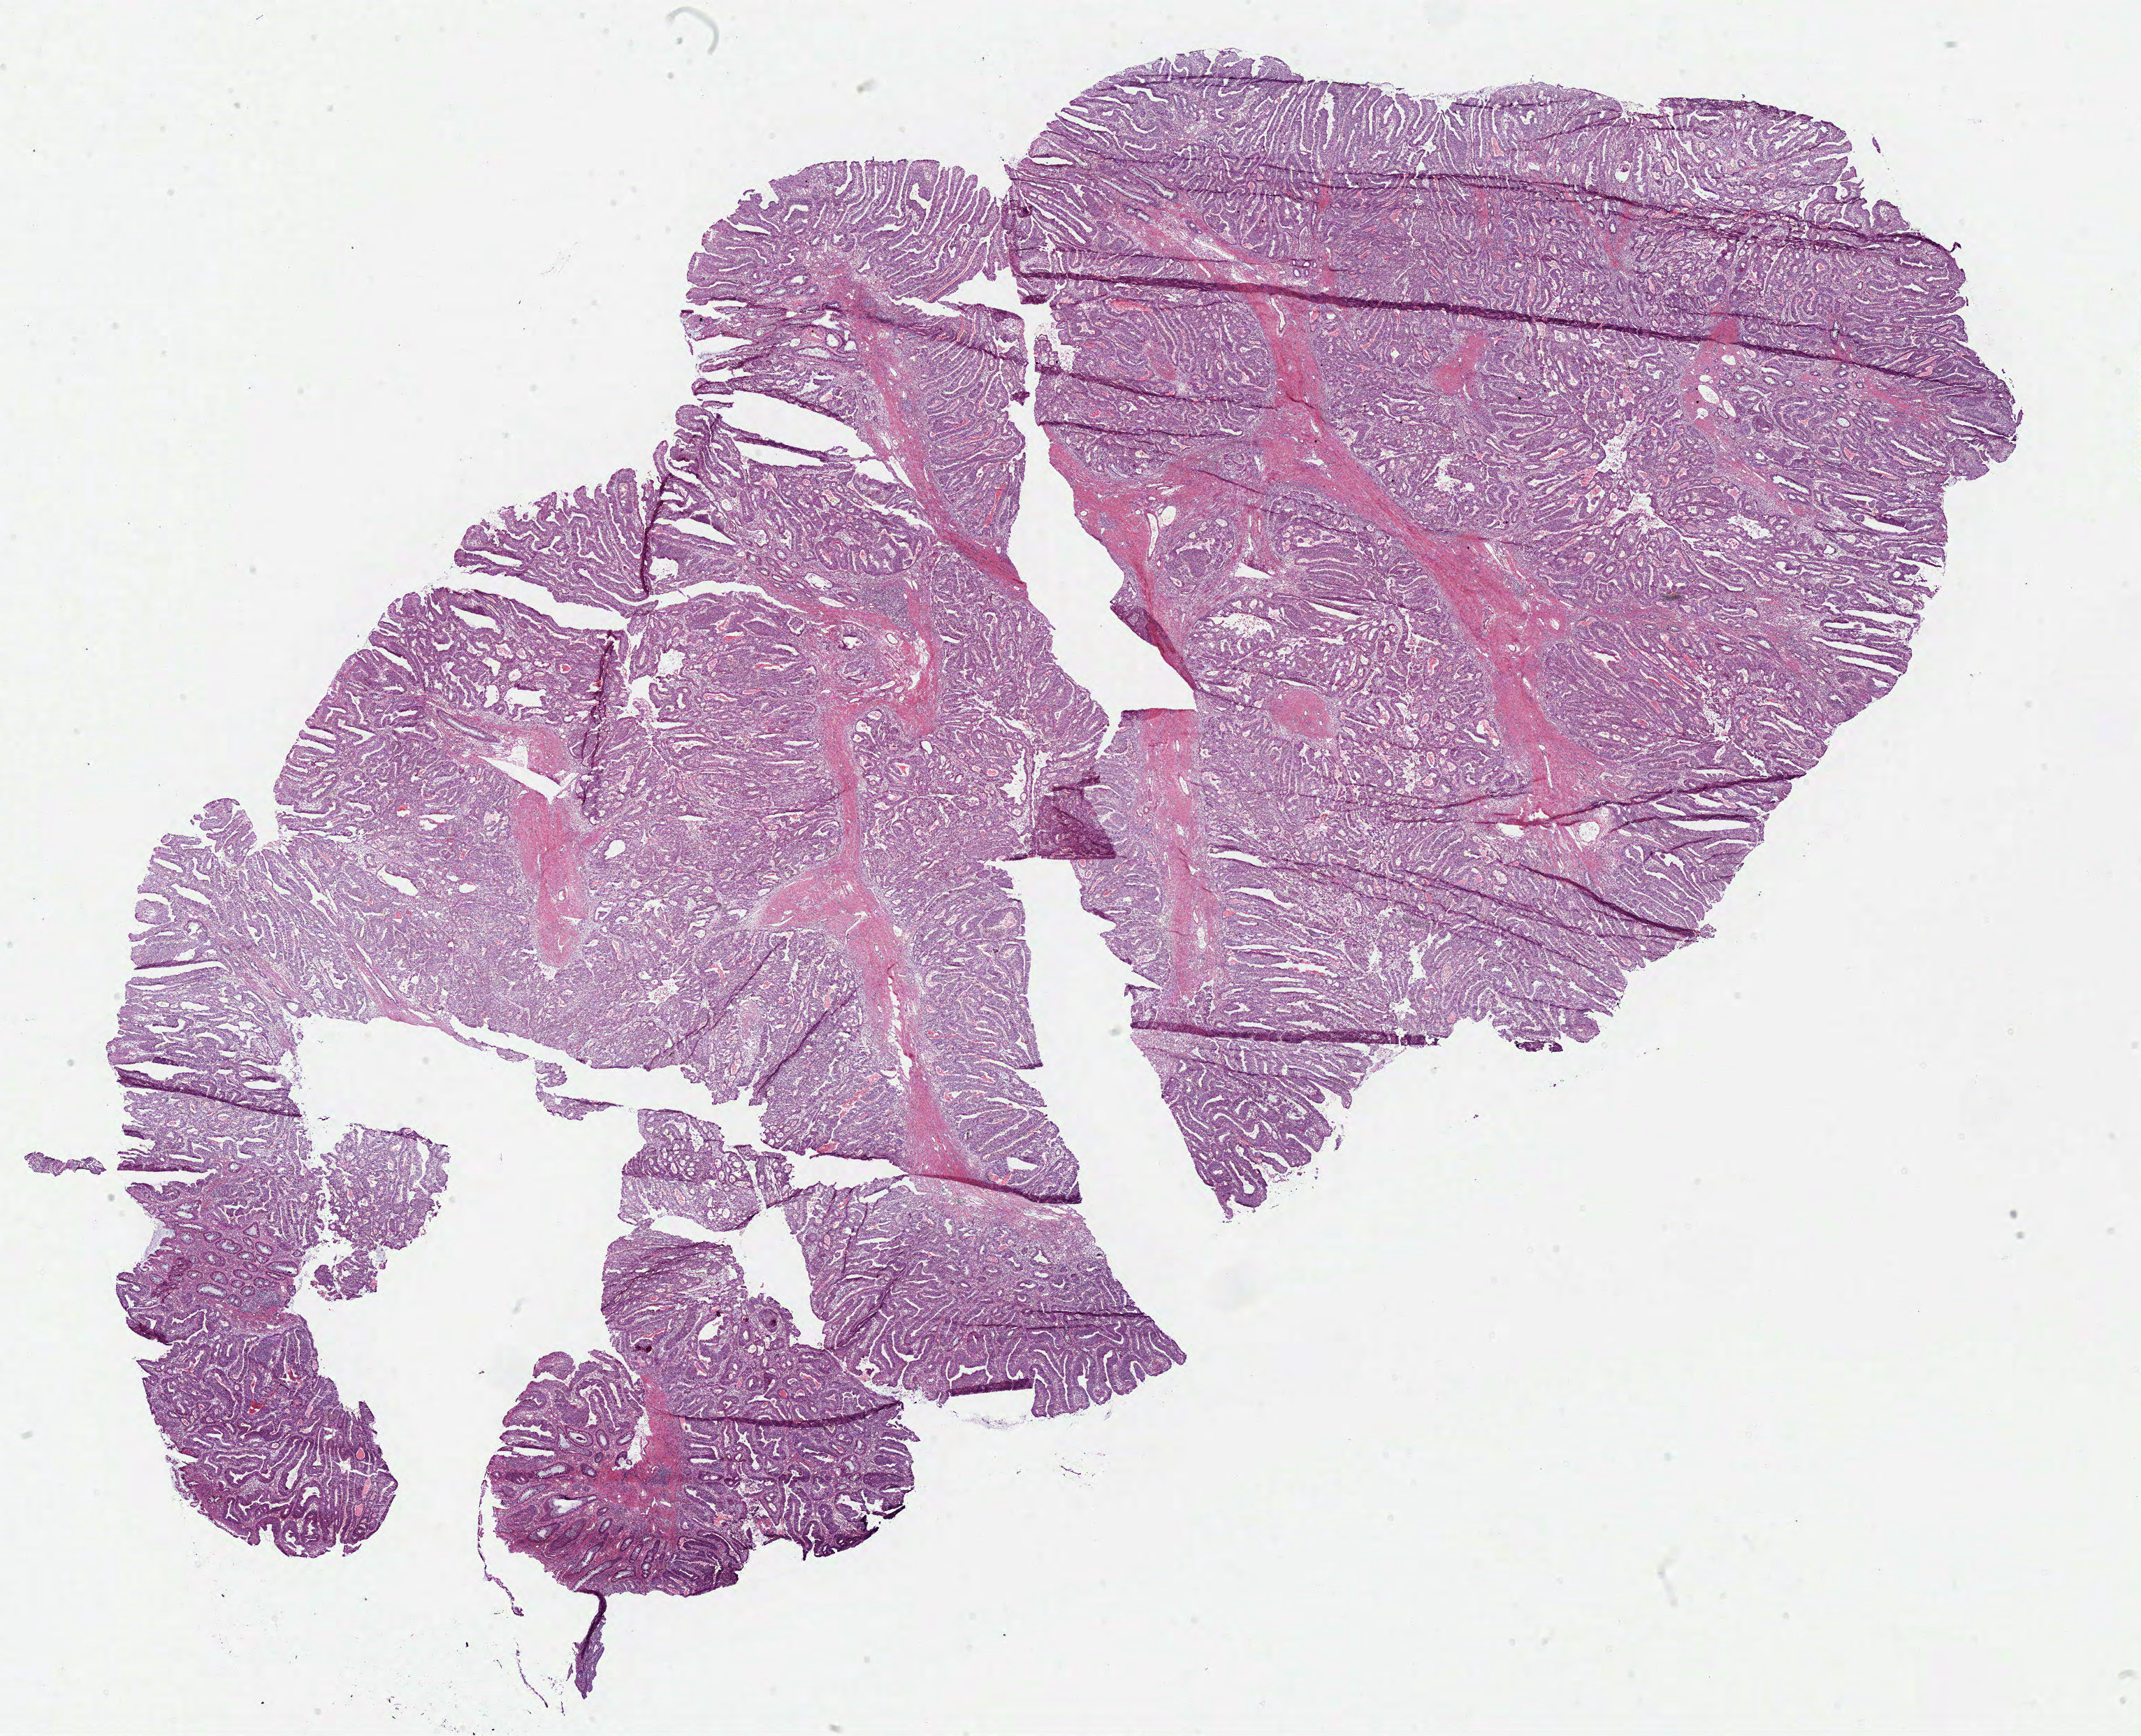
H&E whole-slide image — a low-resolution overview of the entire scanned area, about 24.1 x 19.6 mm (from a 40x scan); frozen section from the bottom of the tissue portion; colon, primary tumour sample. Female patient; age at initial diagnosis 36 years. Pathologist review of this section (percent, as recorded): tumour cells 75%, tumour nuclei 80%, normal cells 5%, stromal cells 10%, necrosis 10%.
* pathologic diagnosis: Adenocarcinoma, NOS (sigmoid colon)
* AJCC pathologic stage: I (7th edition)